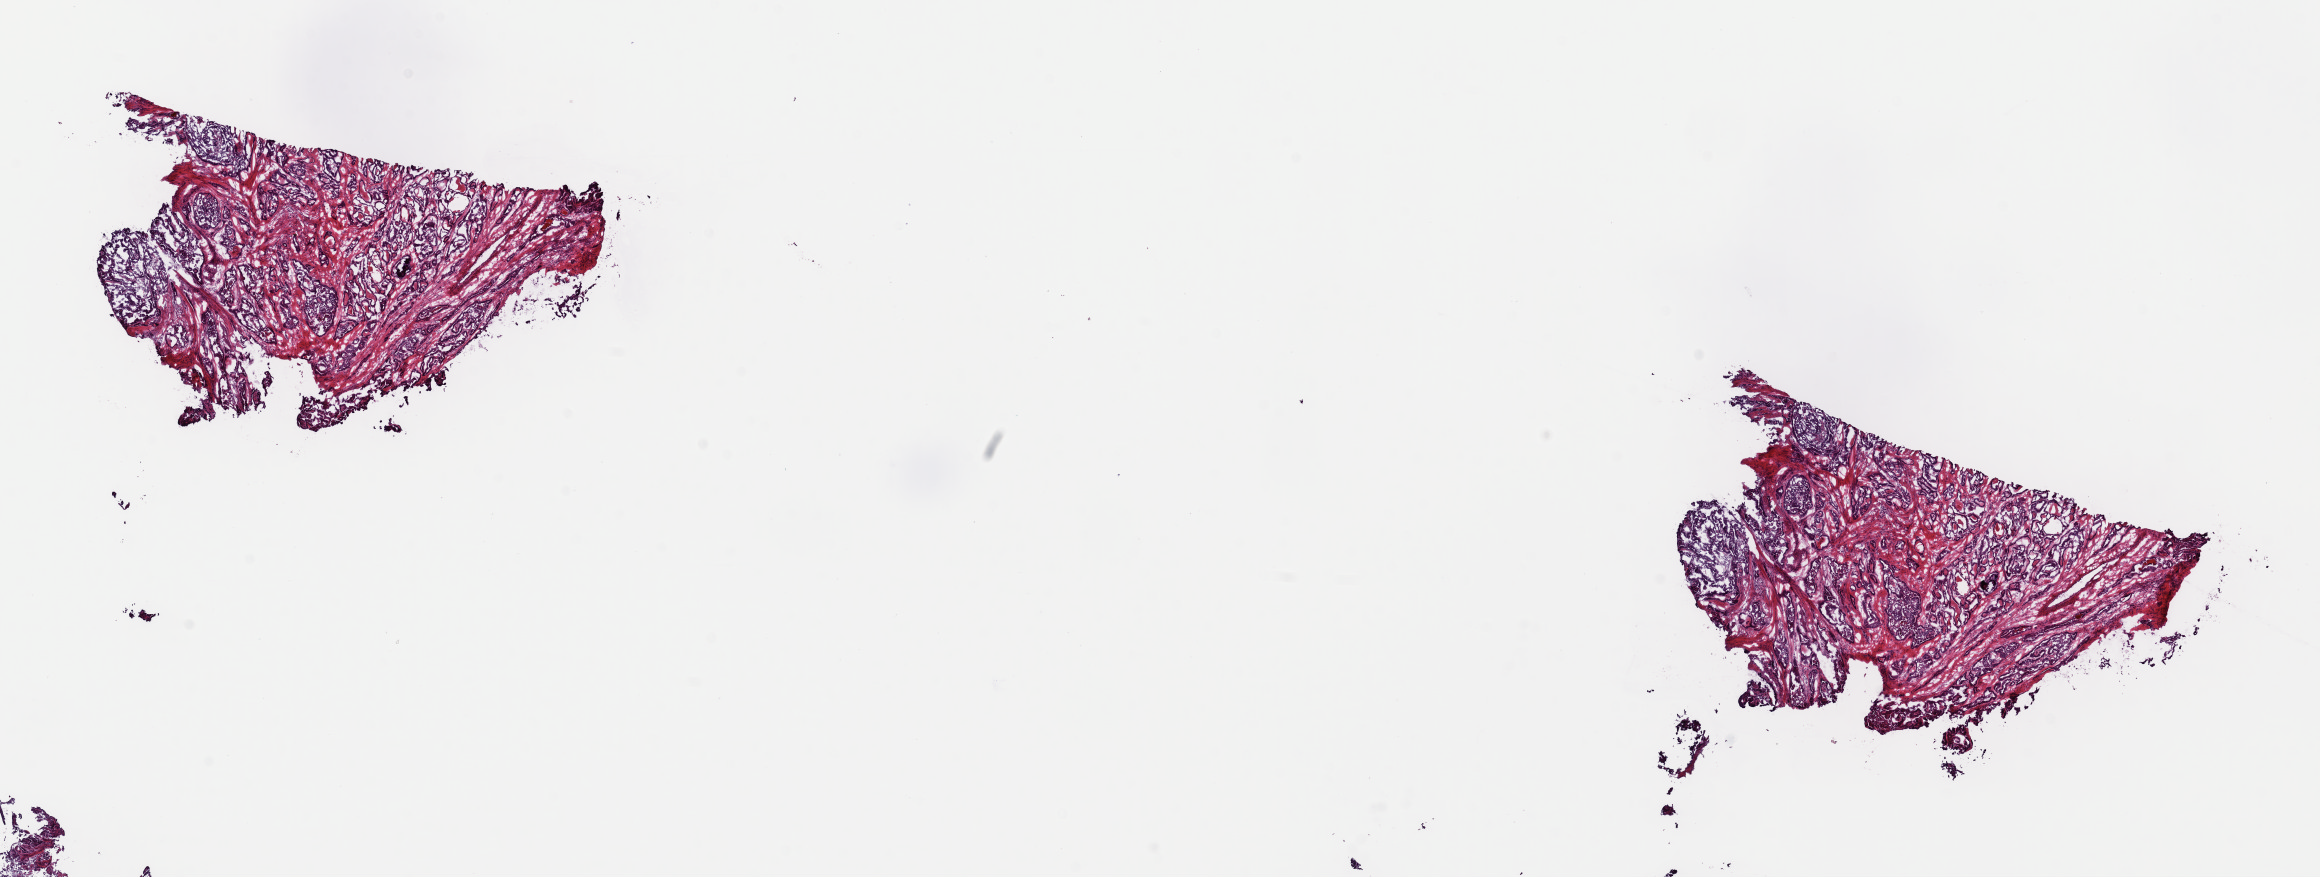
Digitized H&E-stained tissue section (whole slide) — whole scanned area (about 18.3 x 6.9 mm) shown as a low-resolution overview; frozen section; primary tumour sample from the thyroid. Male patient; age at initial diagnosis 81 years. Pathologist review of this section (percent, as recorded): tumour cells 50%, tumour nuclei 100%, normal cells 0%, stromal cells 50%, necrosis 0%. Infiltration values recorded for this section: lymphocyte infiltration 1%, monocyte infiltration 1%, neutrophil infiltration 0%.
AJCC pathologic stage: IVC (6th edition). Pathologic diagnosis: Papillary adenocarcinoma, NOS.